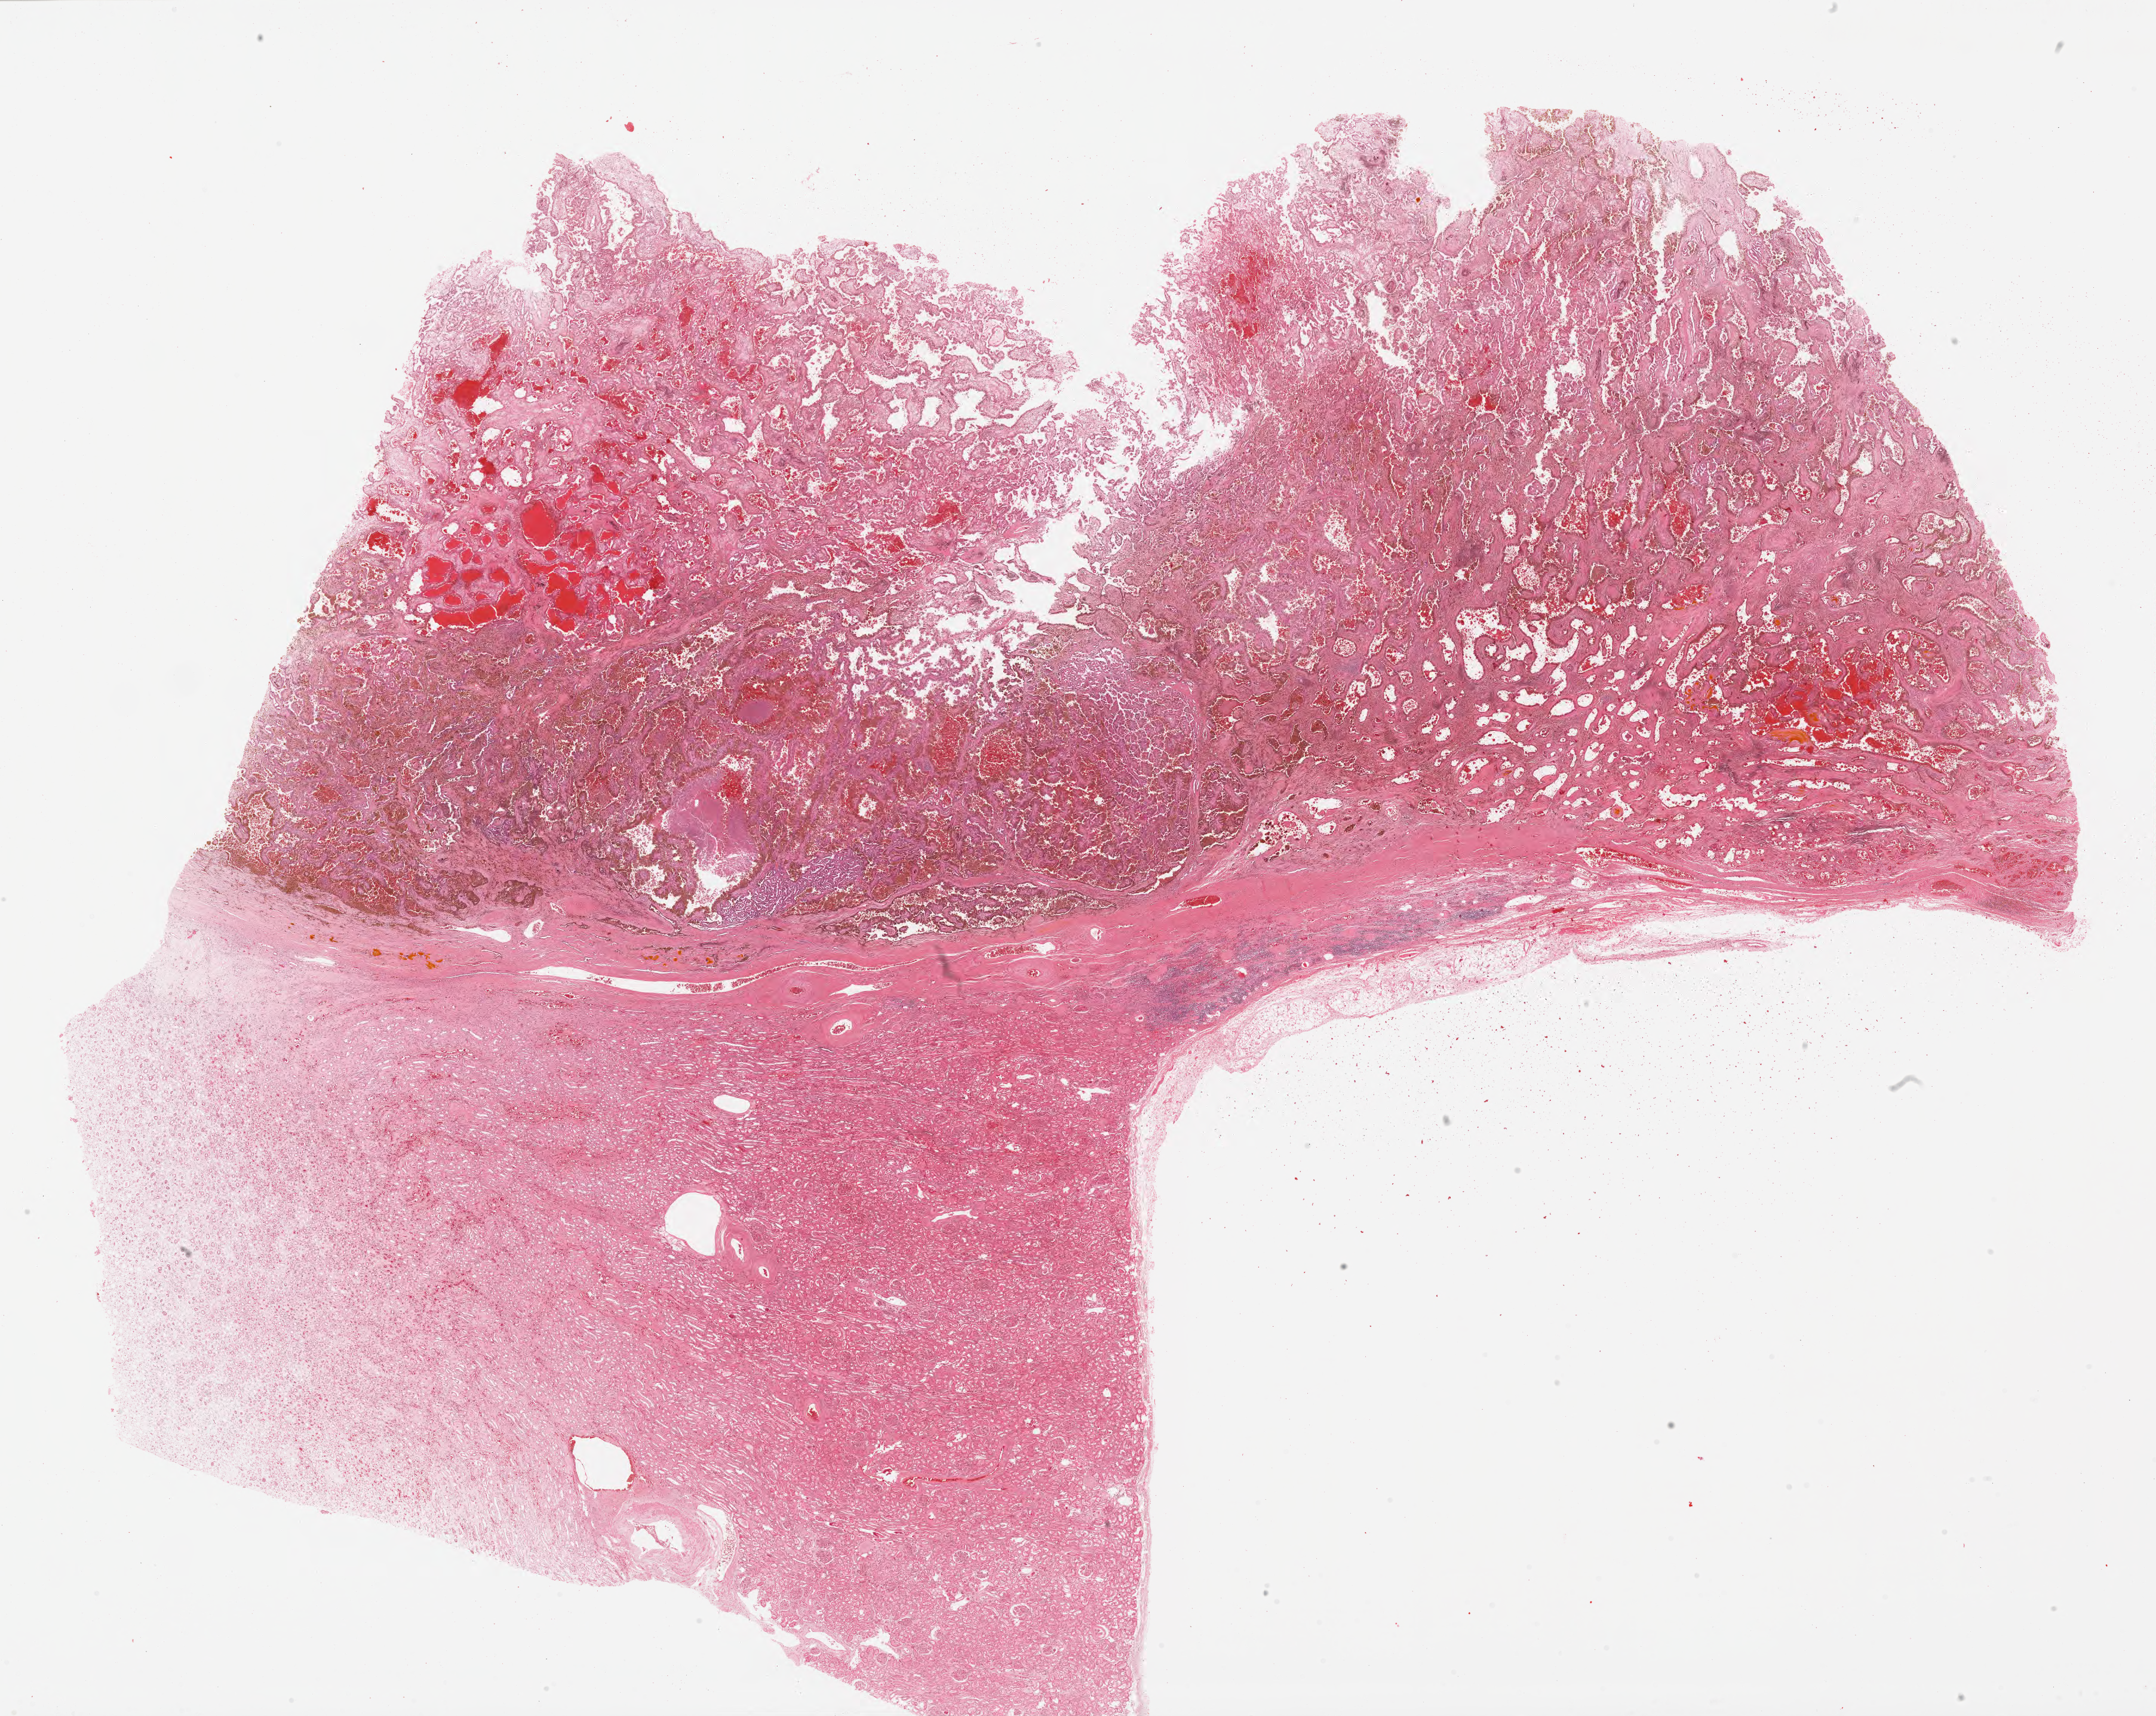
H&E whole-slide image, whole scanned area (about 28.5 x 22.7 mm, from a 20x scan) shown as a low-resolution overview; FFPE section; primary tumour sample from the kidney. Male patient; age at initial diagnosis 63 years.
TNM: T1b NX MX. Pathologic diagnosis: Papillary adenocarcinoma, NOS. Laterality: left. AJCC pathologic stage: I (5th edition).